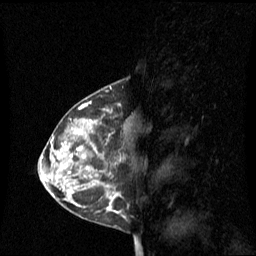
Breast MRI (dynamic contrast-enhanced), one sagittal slice; slice 35 of 60 in the series (ordered by position); dynamic contrast-enhanced series, image 2 of 3 at this slice position (ordered by acquisition); 1.5 T; TE 4.2 ms, TR 8.4 ms; 256 × 256 image matrix, field of view 240 × 240 mm. Patient: female, 42 years. From the clinical record (not read from this slice): setting: breast cancer imaged before/during neoadjuvant chemotherapy; receptor status: HR-positive, HER2-negative.
Annotated regions visible in this slice (semi-automatic segmentation, software-assisted and operator-edited):
- analysis volume of interest (the breast-tissue region the enhancement analysis was run in; not a lesion): bounding box (x1, y1, x2, y2) in pixels: (68, 110, 127, 201)
- tumour enhancement mask (voxels above the 70 % enhancement threshold inside the analysis volume of interest): (108, 186, 119, 201)